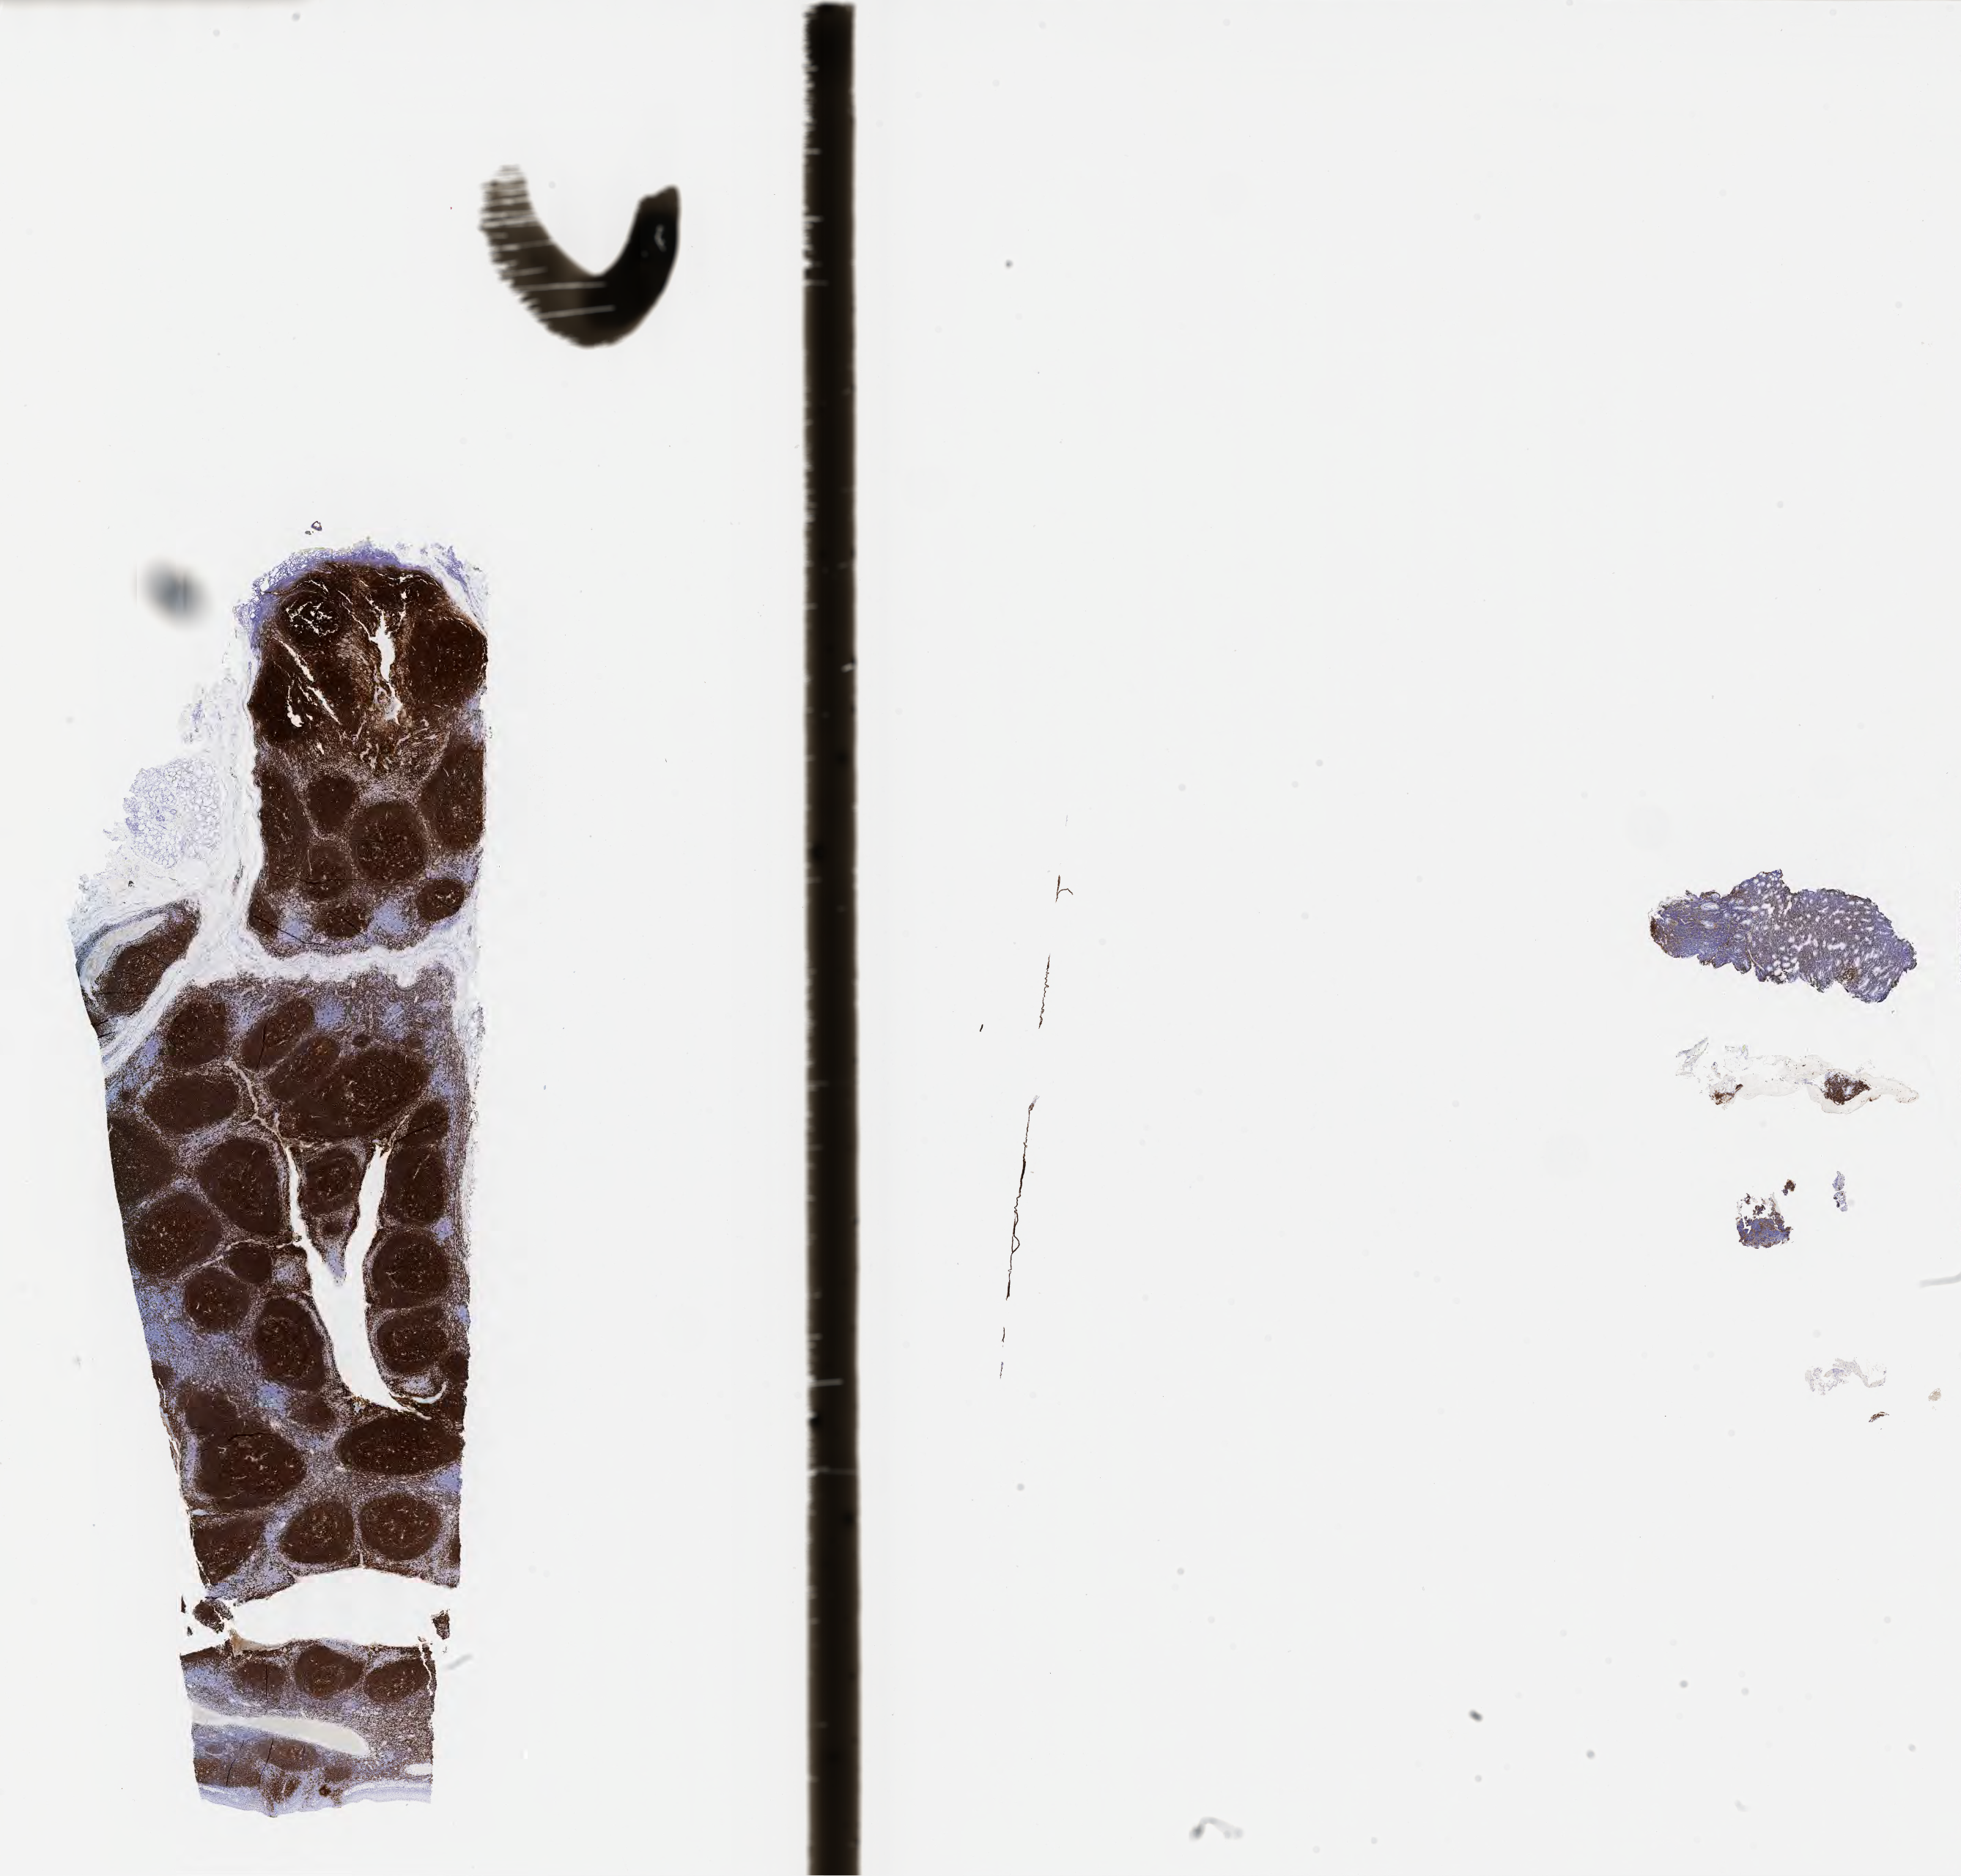
Whole-slide image, immunohistochemical stain for CD20, whole scanned area (about 21.6 x 20.7 mm) shown as a low-resolution overview, specimen: tumor tissue, site: stomach. Patient female; aged 28.
* histologic diagnosis: Burkitt lymphoma, NOS